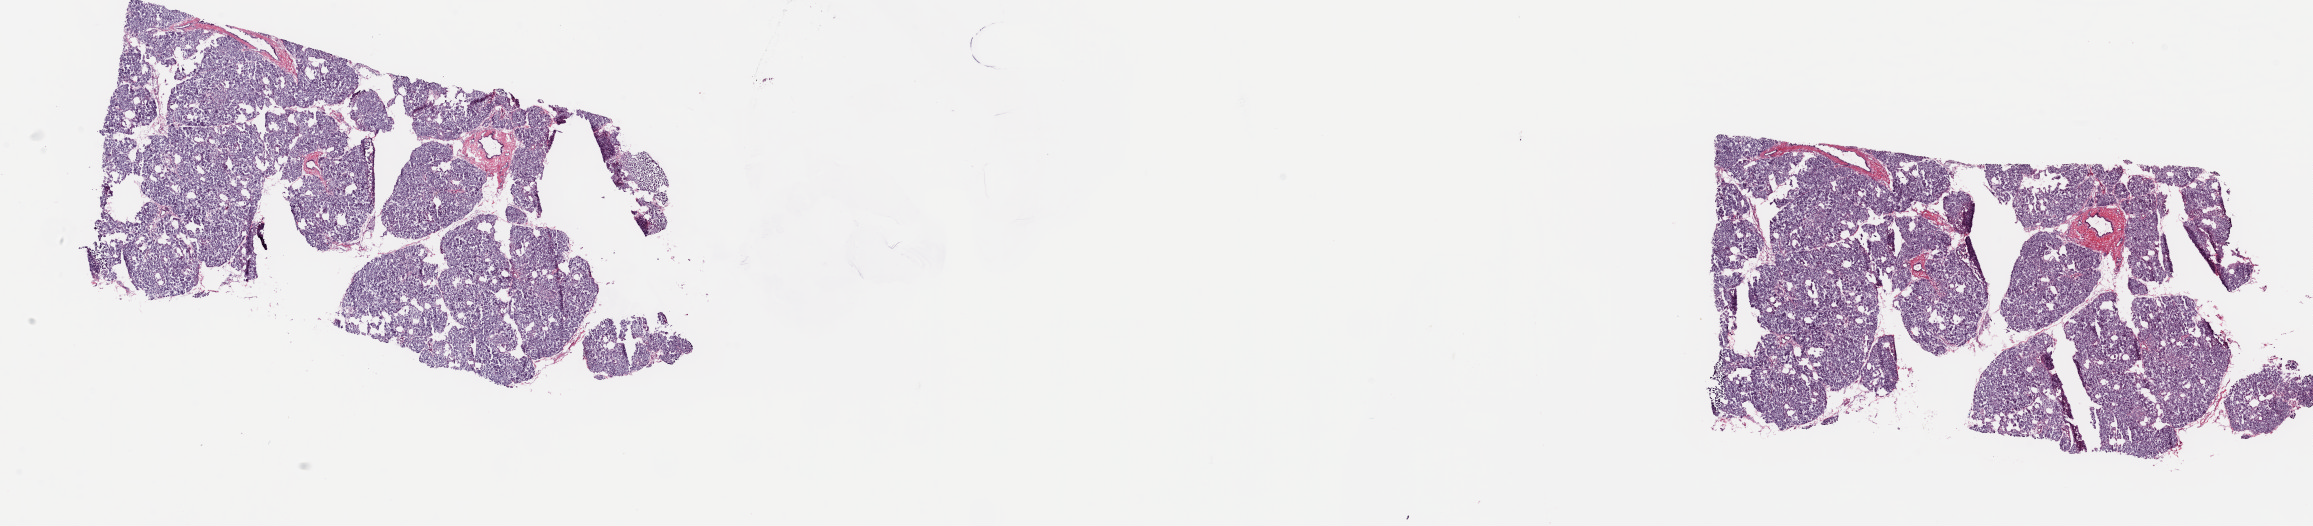
H&E-stained whole-slide image, shown as a low-resolution overview of the whole scanned area (about 36.7 x 8.3 mm); frozen section from the top of the tissue portion; solid tissue normal (non-tumour tissue) sample from the pancreas. Female, age 48 years at initial diagnosis. Composition of this section per pathologist review: tumour cells 0%, tumour nuclei 0%, normal cells 88%, stromal cells 12%, necrosis 0%. Inflammatory infiltration, as recorded: lymphocyte infiltration 2%, monocyte infiltration 1%, neutrophil infiltration 1%.
• this section: solid tissue normal (non-tumour) sample from the same patient
• patient diagnosis: Infiltrating duct carcinoma, NOS (head of pancreas)